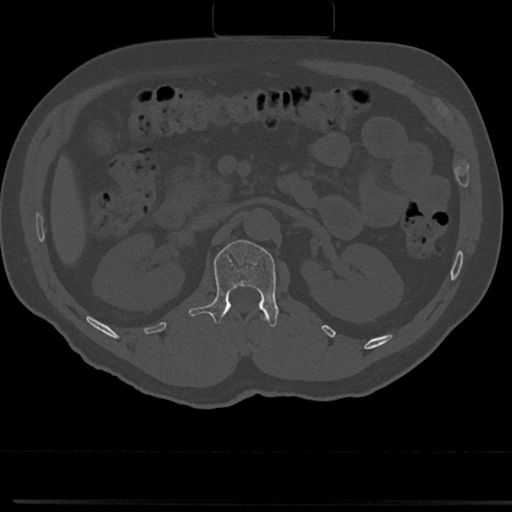
CT including the spine, one axial slice. Position 94 of 817 along the scan axis. Bone window (W 1800 / L 400 HU). 0.5 mm slice thickness. 512 × 512 image matrix, field of view 355 × 355 mm. Patient: male, 61 years. From the clinical record (not read from this slice): primary cancer: prostate.
Annotated regions visible in this slice (semi-automatically segmented with operator editing):
- L1 vertebra: bounding box (x1, y1, x2, y2) in pixels: (191, 240, 279, 327)